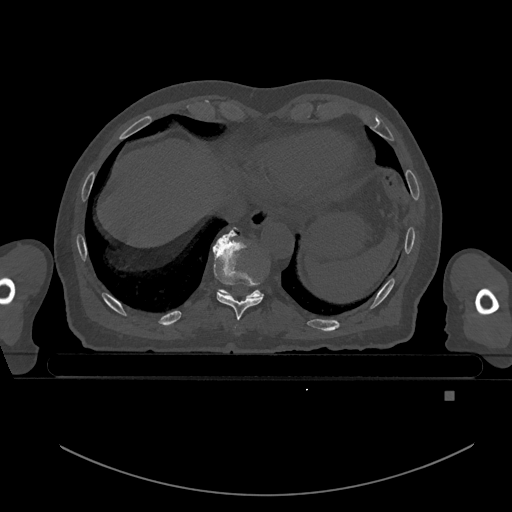
CT including the spine, one axial slice; slice 131 of 969 in the series (ordered by position); bone window (W 1800 / L 400 HU); 512 × 512 image matrix, field of view 456 × 456 mm. Patient: male, 82 years. From the clinical record (not read from this slice): primary cancer: prostate; vertebrae with lytic lesions (as recorded): T11, T9, T8, T2.
Outlined on this slice (semi-automatically segmented with operator editing):
- T10 vertebra: bounding box (x1, y1, x2, y2) in pixels: (220, 227, 261, 297)
- T8 vertebra: (235, 325, 237, 329)
- T9 vertebra: (213, 230, 266, 320)